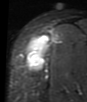
MRI of an extremity soft-tissue mass, one axial slice; position 33 of 48 along the scan axis; STIR; MR volume resampled by the dataset authors to the PET/CT grid (not the native acquisition matrix); 3.27 mm slice thickness; 87 × 102 image matrix, field of view 85 × 100 mm. Female patient. From the clinical record (not read from this slice): histological type: synovial sarcoma; grade: intermediate; site of the primary tumour: right thigh.
Outlined on this slice (expert contour drawn on MRI and transferred to this co-registered scan by the dataset authors):
- gross tumour volume including surrounding oedema: bounding box <28,34,54,69> (left, top, right, bottom; pixels)
- gross tumour volume (mass): <26,36,48,69>